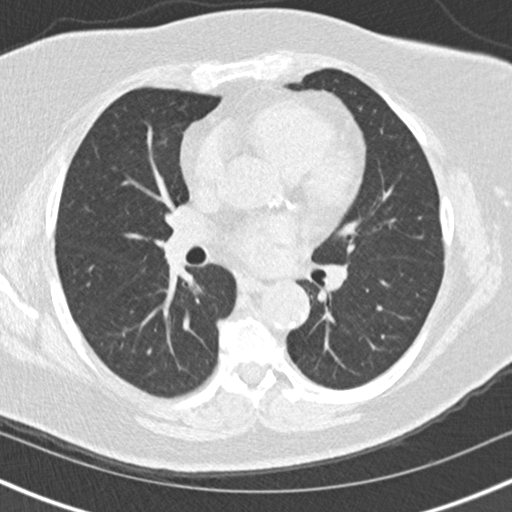
Low-dose screening chest CT, one axial slice; reconstruction kernel B30f; 120 kVp; lung window (W 1500 / L -600 HU); 2 mm slice thickness; 512 × 512 image matrix, field of view 320 × 320 mm.
Outlined on this slice (manually delineated by an expert):
- lesion 1 (tumor, lower lobe of right lung): bounding box [x1, y1, x2, y2] px = [189, 283, 202, 294]